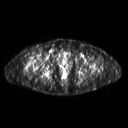
FDG PET of an extremity soft-tissue mass (from a PET/CT study), one axial slice. Position 286 of 311 along the scan axis. 3.27 mm slice thickness. 128 × 128 image matrix, field of view 500 × 500 mm. Female patient, age 57 years. Case-level facts recorded for this patient, not image findings: histological type: pleiomorphic undifferentiated sarcoma; grade: high; site of the primary tumour: right quadricep.
Annotated regions visible in this slice (expert contour drawn on MRI and transferred to this co-registered scan by the dataset authors):
- tumour plus oedema (research contour): bounding box [x1, y1, x2, y2] px = [27, 57, 34, 67]